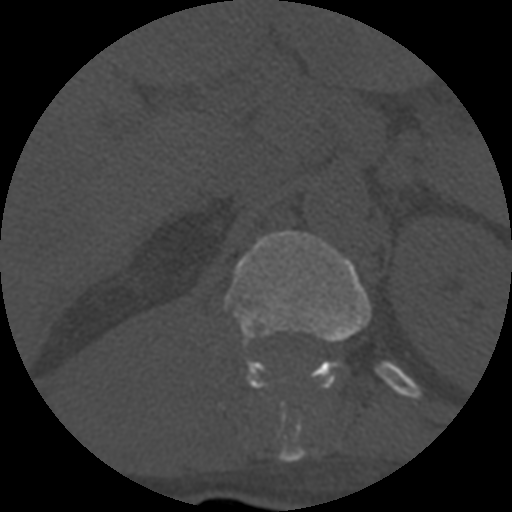
CT including the spine, one axial slice; slice 309 of 708 in the series (ordered by position); reconstruction kernel STANDARD; 120 kVp; one of 3 acquisitions stored at this slice position; bone window (W 1800 / L 400 HU); 512 × 512 image matrix, field of view 160 × 160 mm. Patient age 55 years. From the clinical record (not read from this slice): primary cancer: colon; vertebrae with lytic lesions (as recorded): T12, L1, L5.
Annotated regions visible in this slice (semi-automatic segmentation, software-assisted and operator-edited):
- T12 vertebra: bounding box <224,231,371,462> (left, top, right, bottom; pixels)